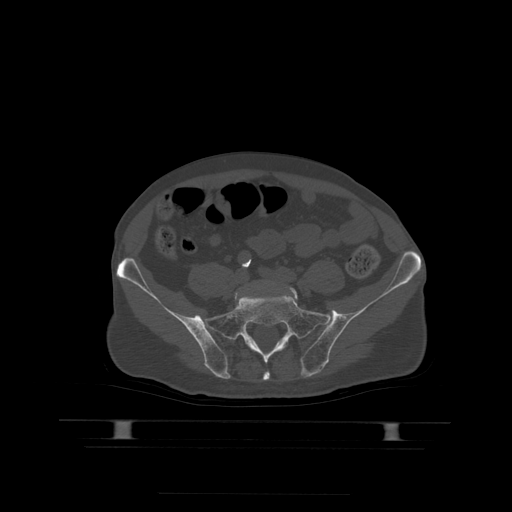
CT including the spine, one axial slice. Position 54 of 522 along the scan axis. Bone window (W 1800 / L 400 HU). 512 × 512 image matrix, field of view 436 × 436 mm. Patient age 68 years. From the clinical record (not read from this slice): primary cancer: urothelial.
Annotated regions visible in this slice (semi-automatic segmentation, software-assisted and operator-edited):
- L5 vertebra: bounding box <290,288,298,300> (left, top, right, bottom; pixels)